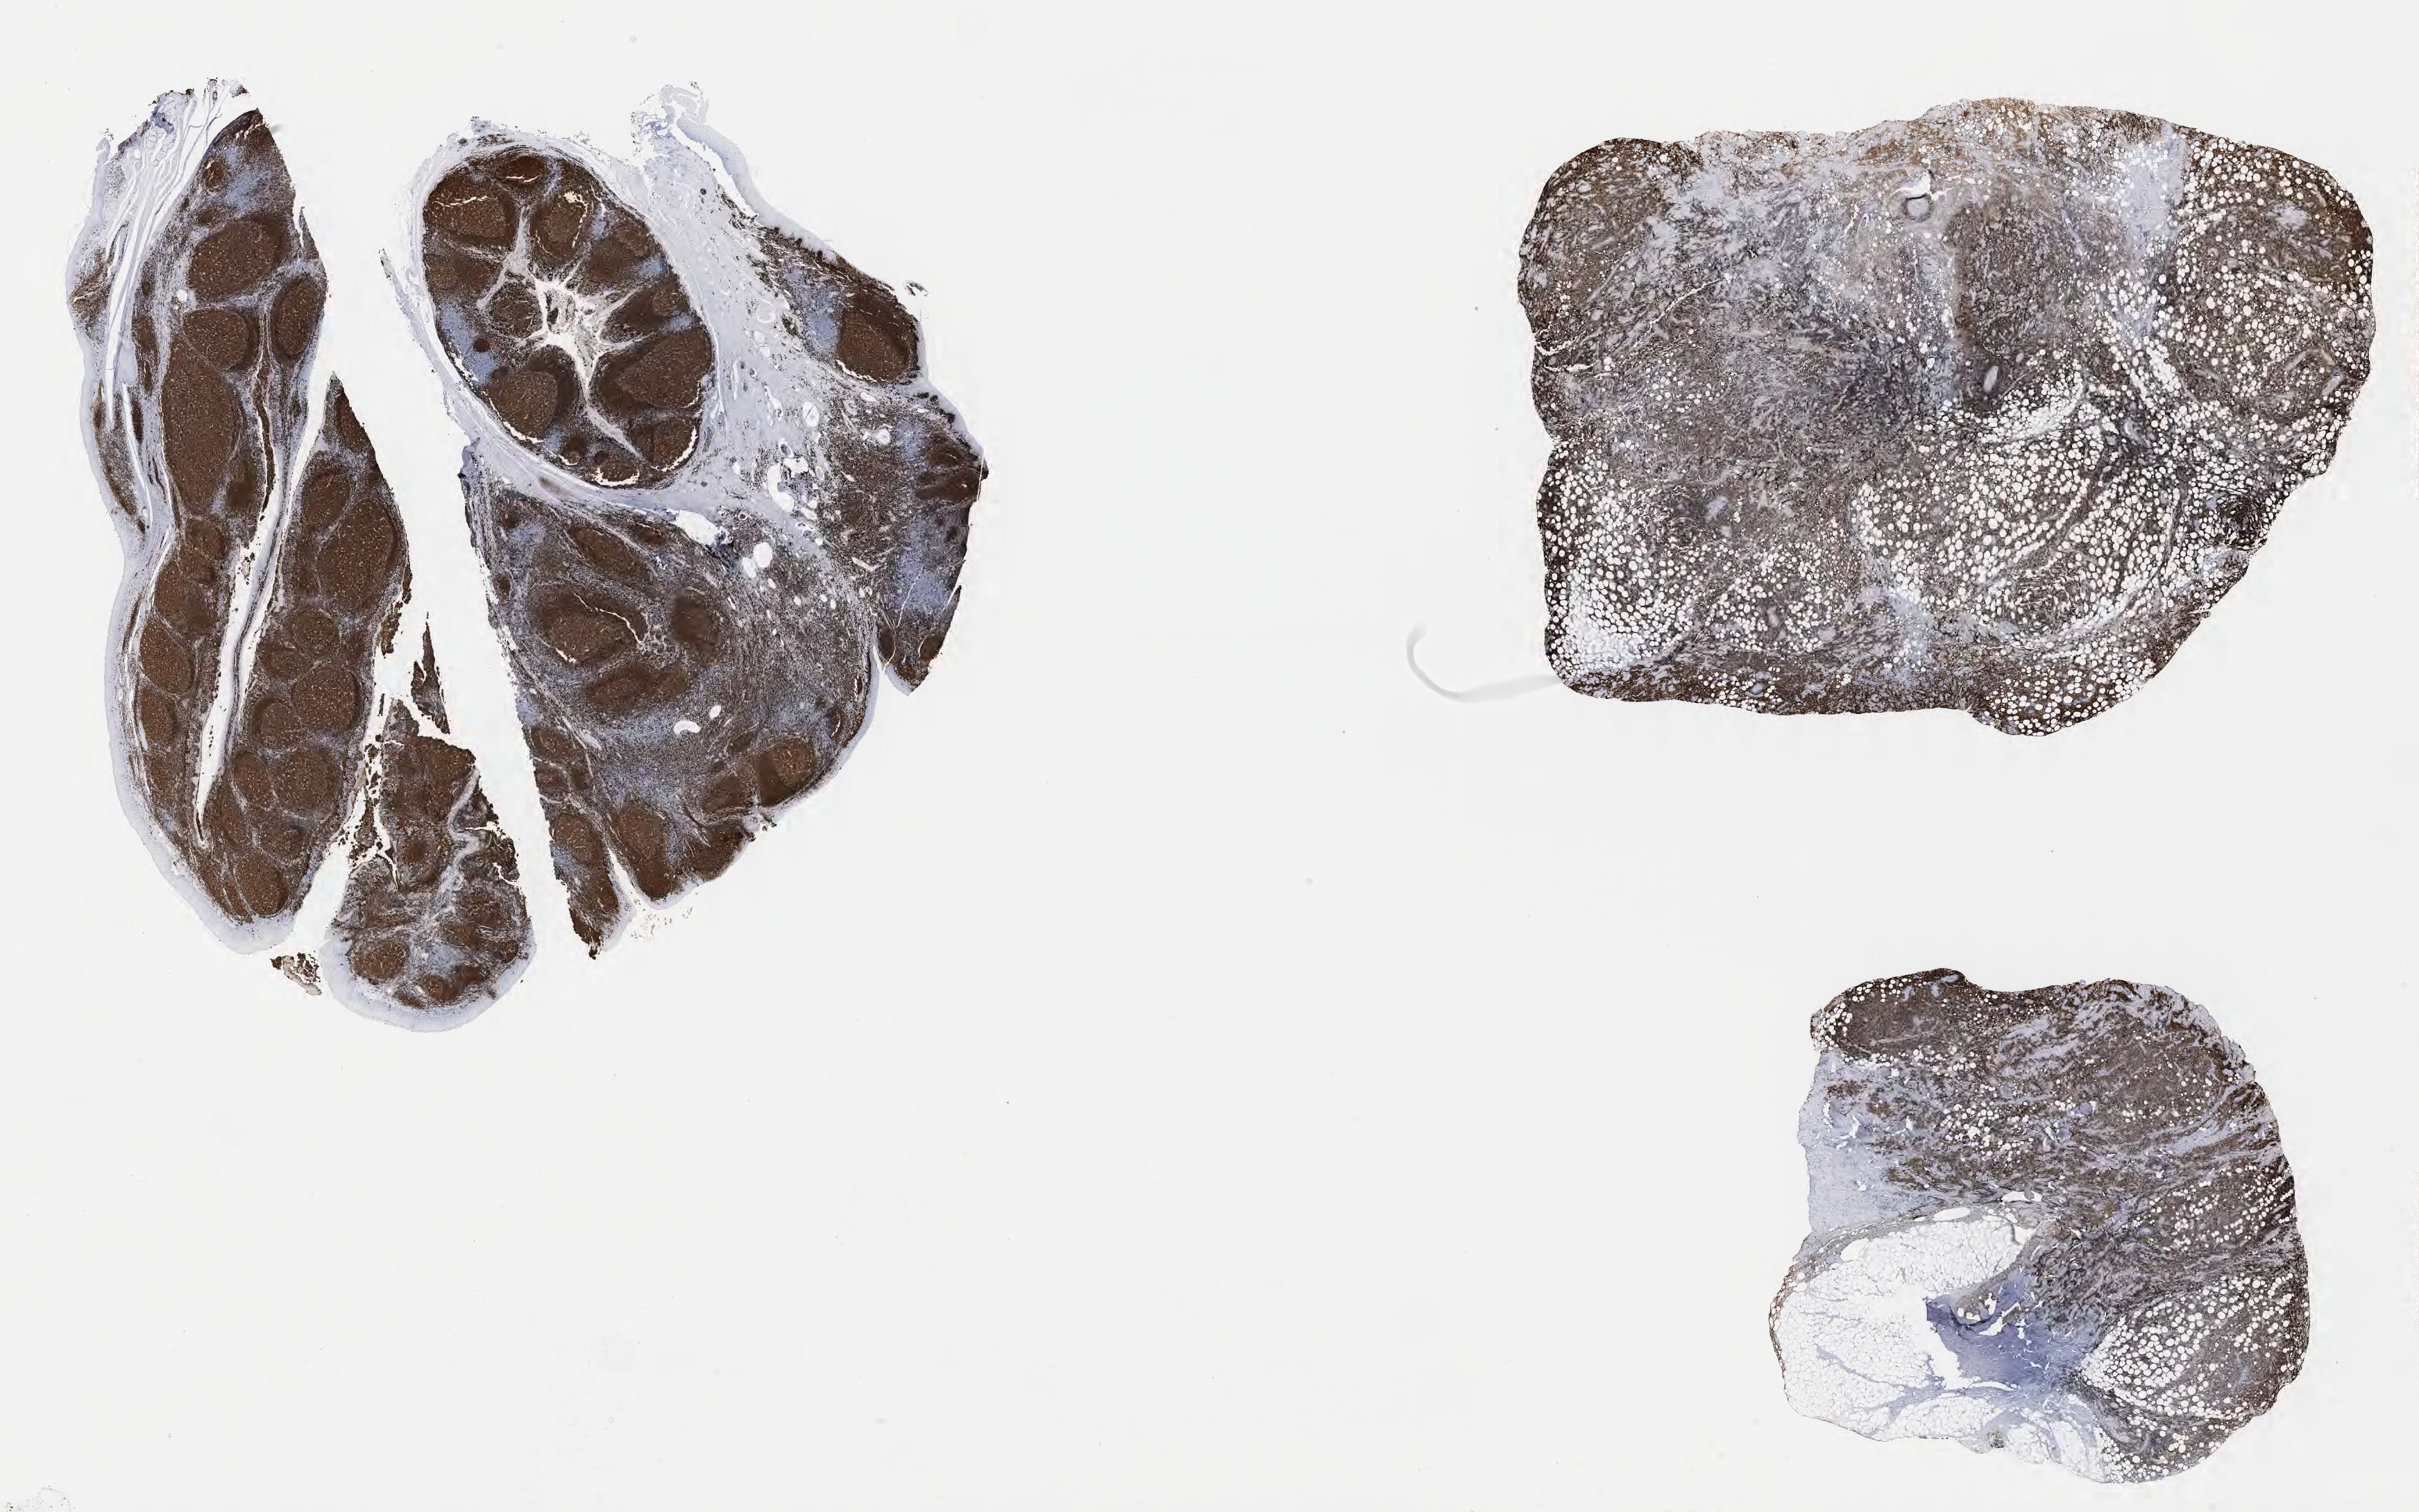
IHC for CD79a, whole-slide image, low-resolution overview of the scanned area, about 28.2 x 17.6 mm. Tumor tissue. Anatomic site: kidney. Male patient, 63 years old.
Histologic diagnosis: Diffuse large B-cell lymphoma, NOS.